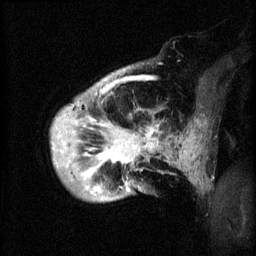
Breast MRI (dynamic contrast-enhanced), one sagittal slice; slice 7 of 60 in the series (ordered by position); 3 images stored at this slice position (order not interpretable as contrast timing); 1.5 T; TE 4.2 ms, TR 8.2 ms; 2 mm slice thickness; 256 × 256 image matrix, field of view 200 × 200 mm. Female patient, age 50 years.
Outlined on this slice (semi-automatic segmentation, software-assisted and operator-edited):
- analysis volume of interest (the breast-tissue region the enhancement analysis was run in; not a lesion): bounding box <51,72,170,203> (left, top, right, bottom; pixels)
- tumour enhancement mask (voxels above the 70 % enhancement threshold inside the analysis volume of interest): <54,80,169,191>